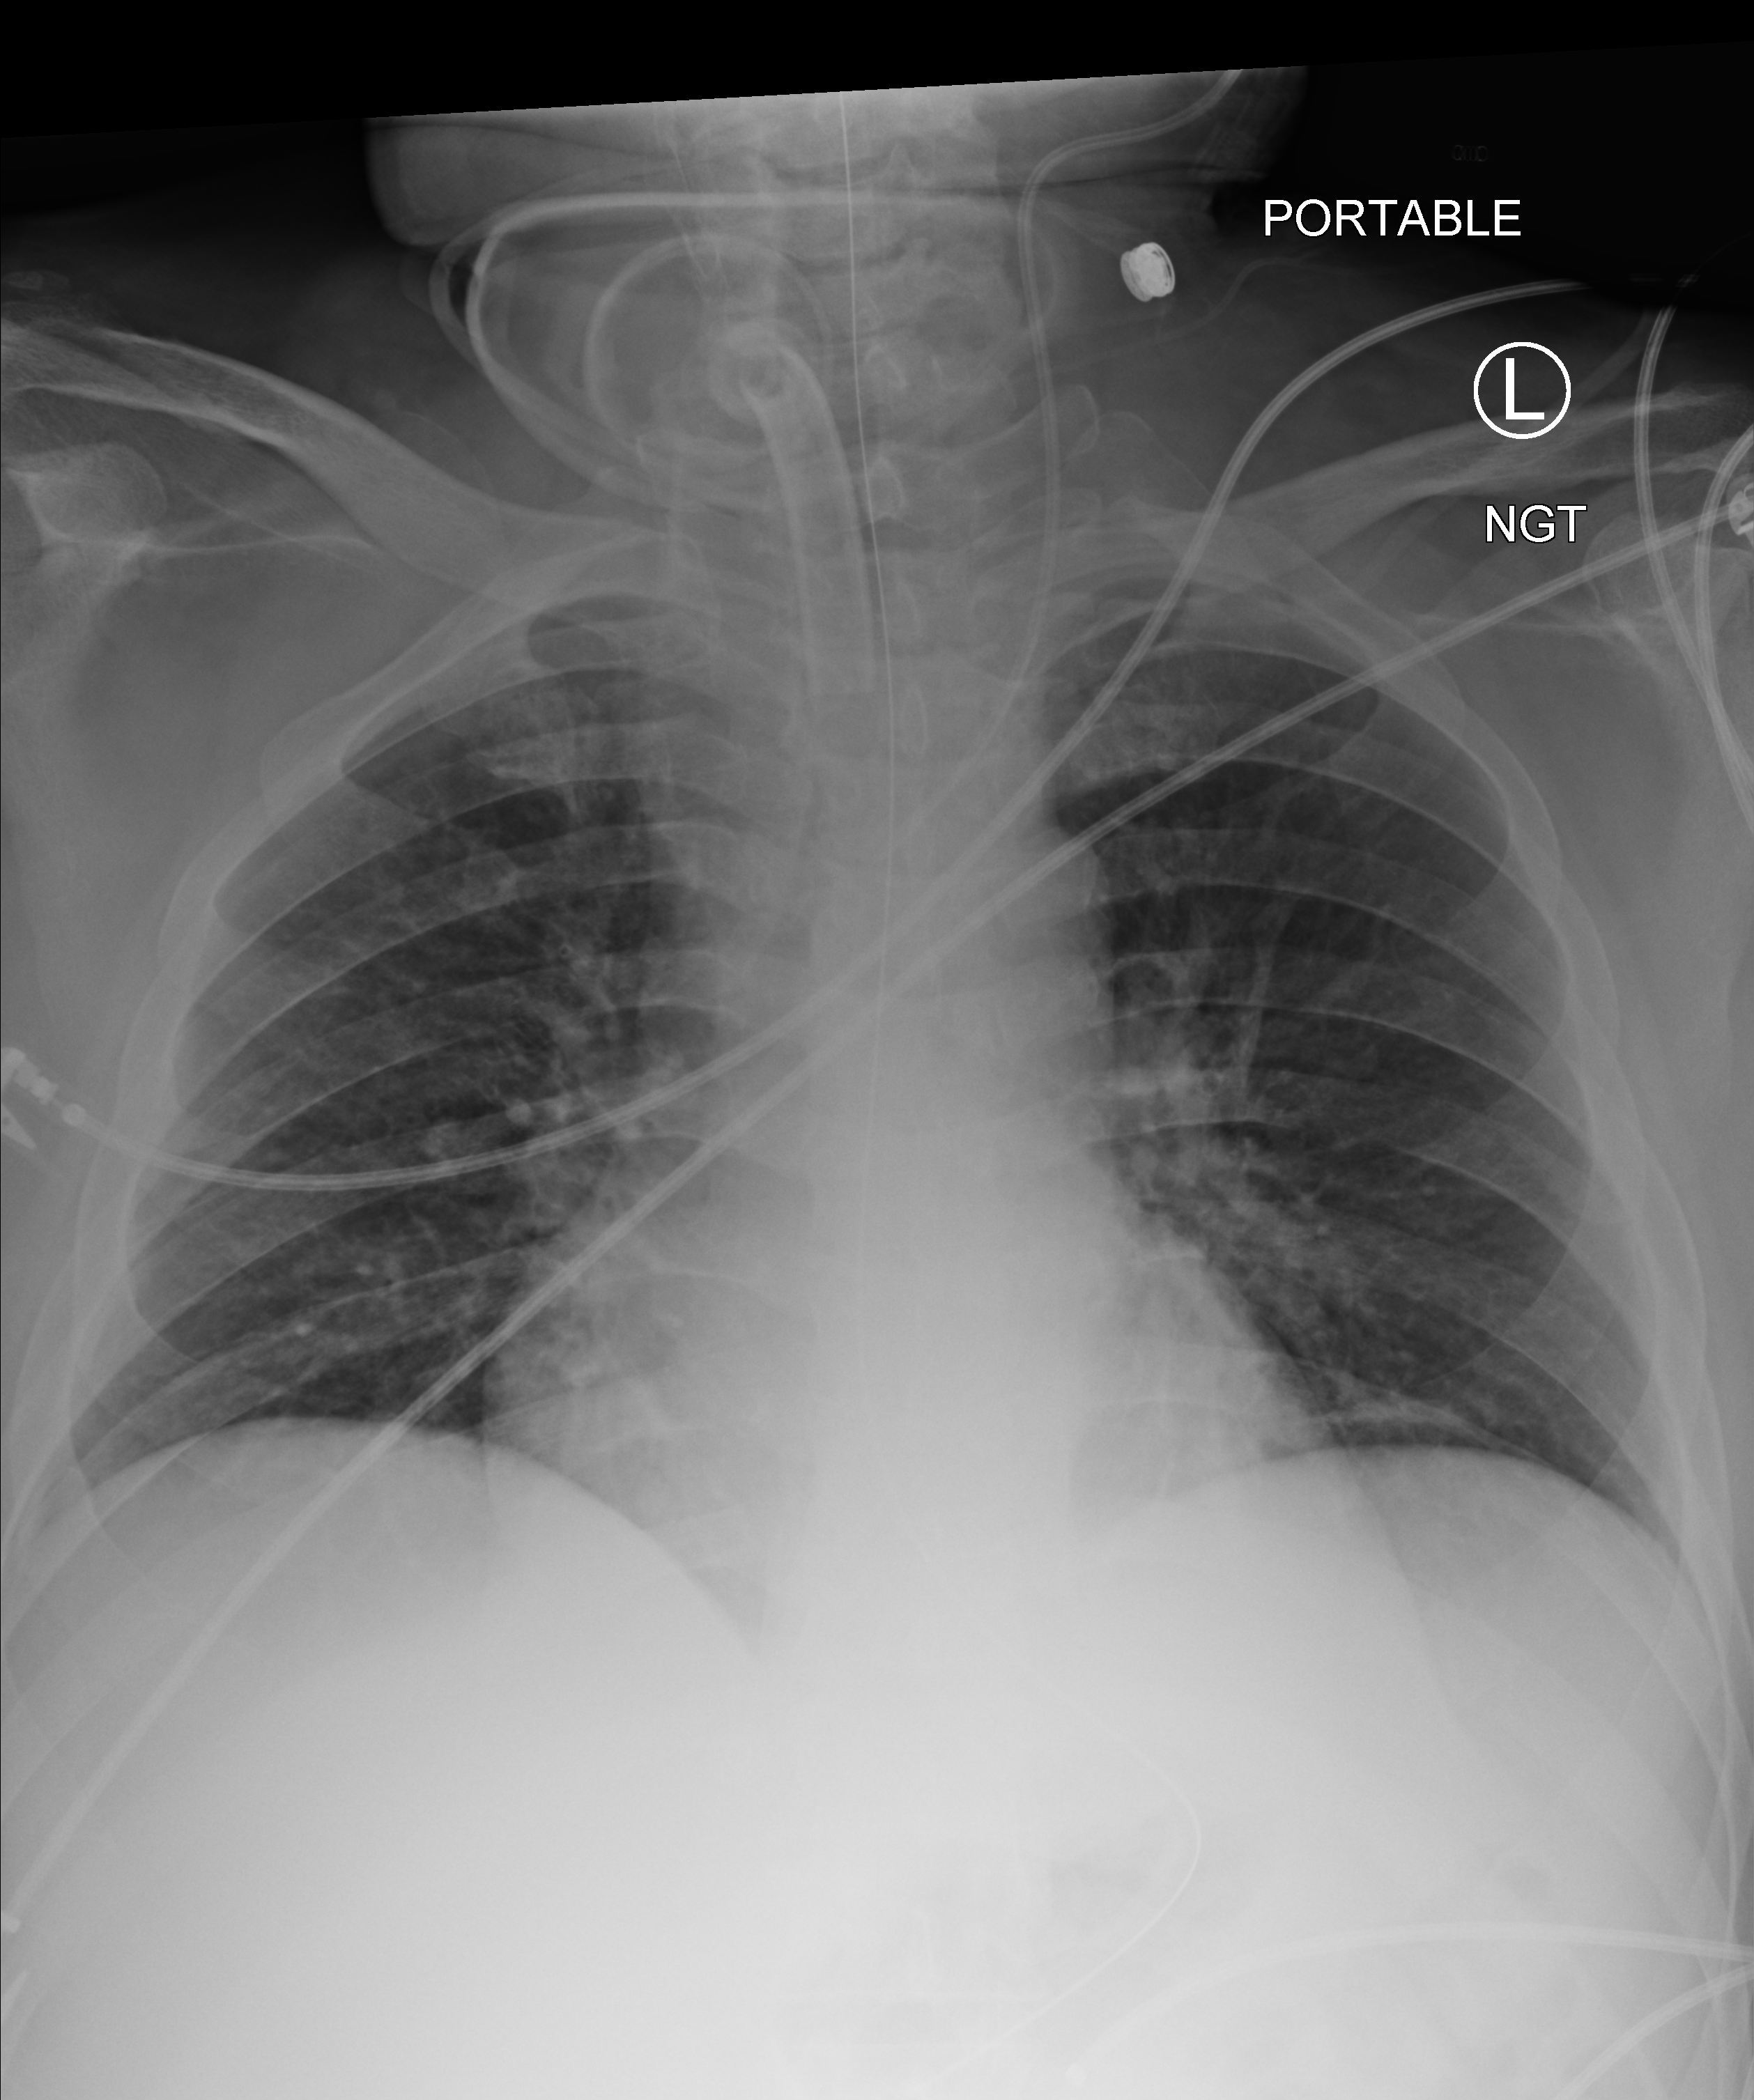
Portable chest radiograph. Male patient hospitalised with COVID-19, age 18–59 years.
From the hospital-stay record, not from the radiograph (when in the stay this image was taken is not recorded):
- mechanically ventilated during this hospital stay: yes
- admitted to intensive care during this hospital stay: yes
- length of hospital stay: 65 days